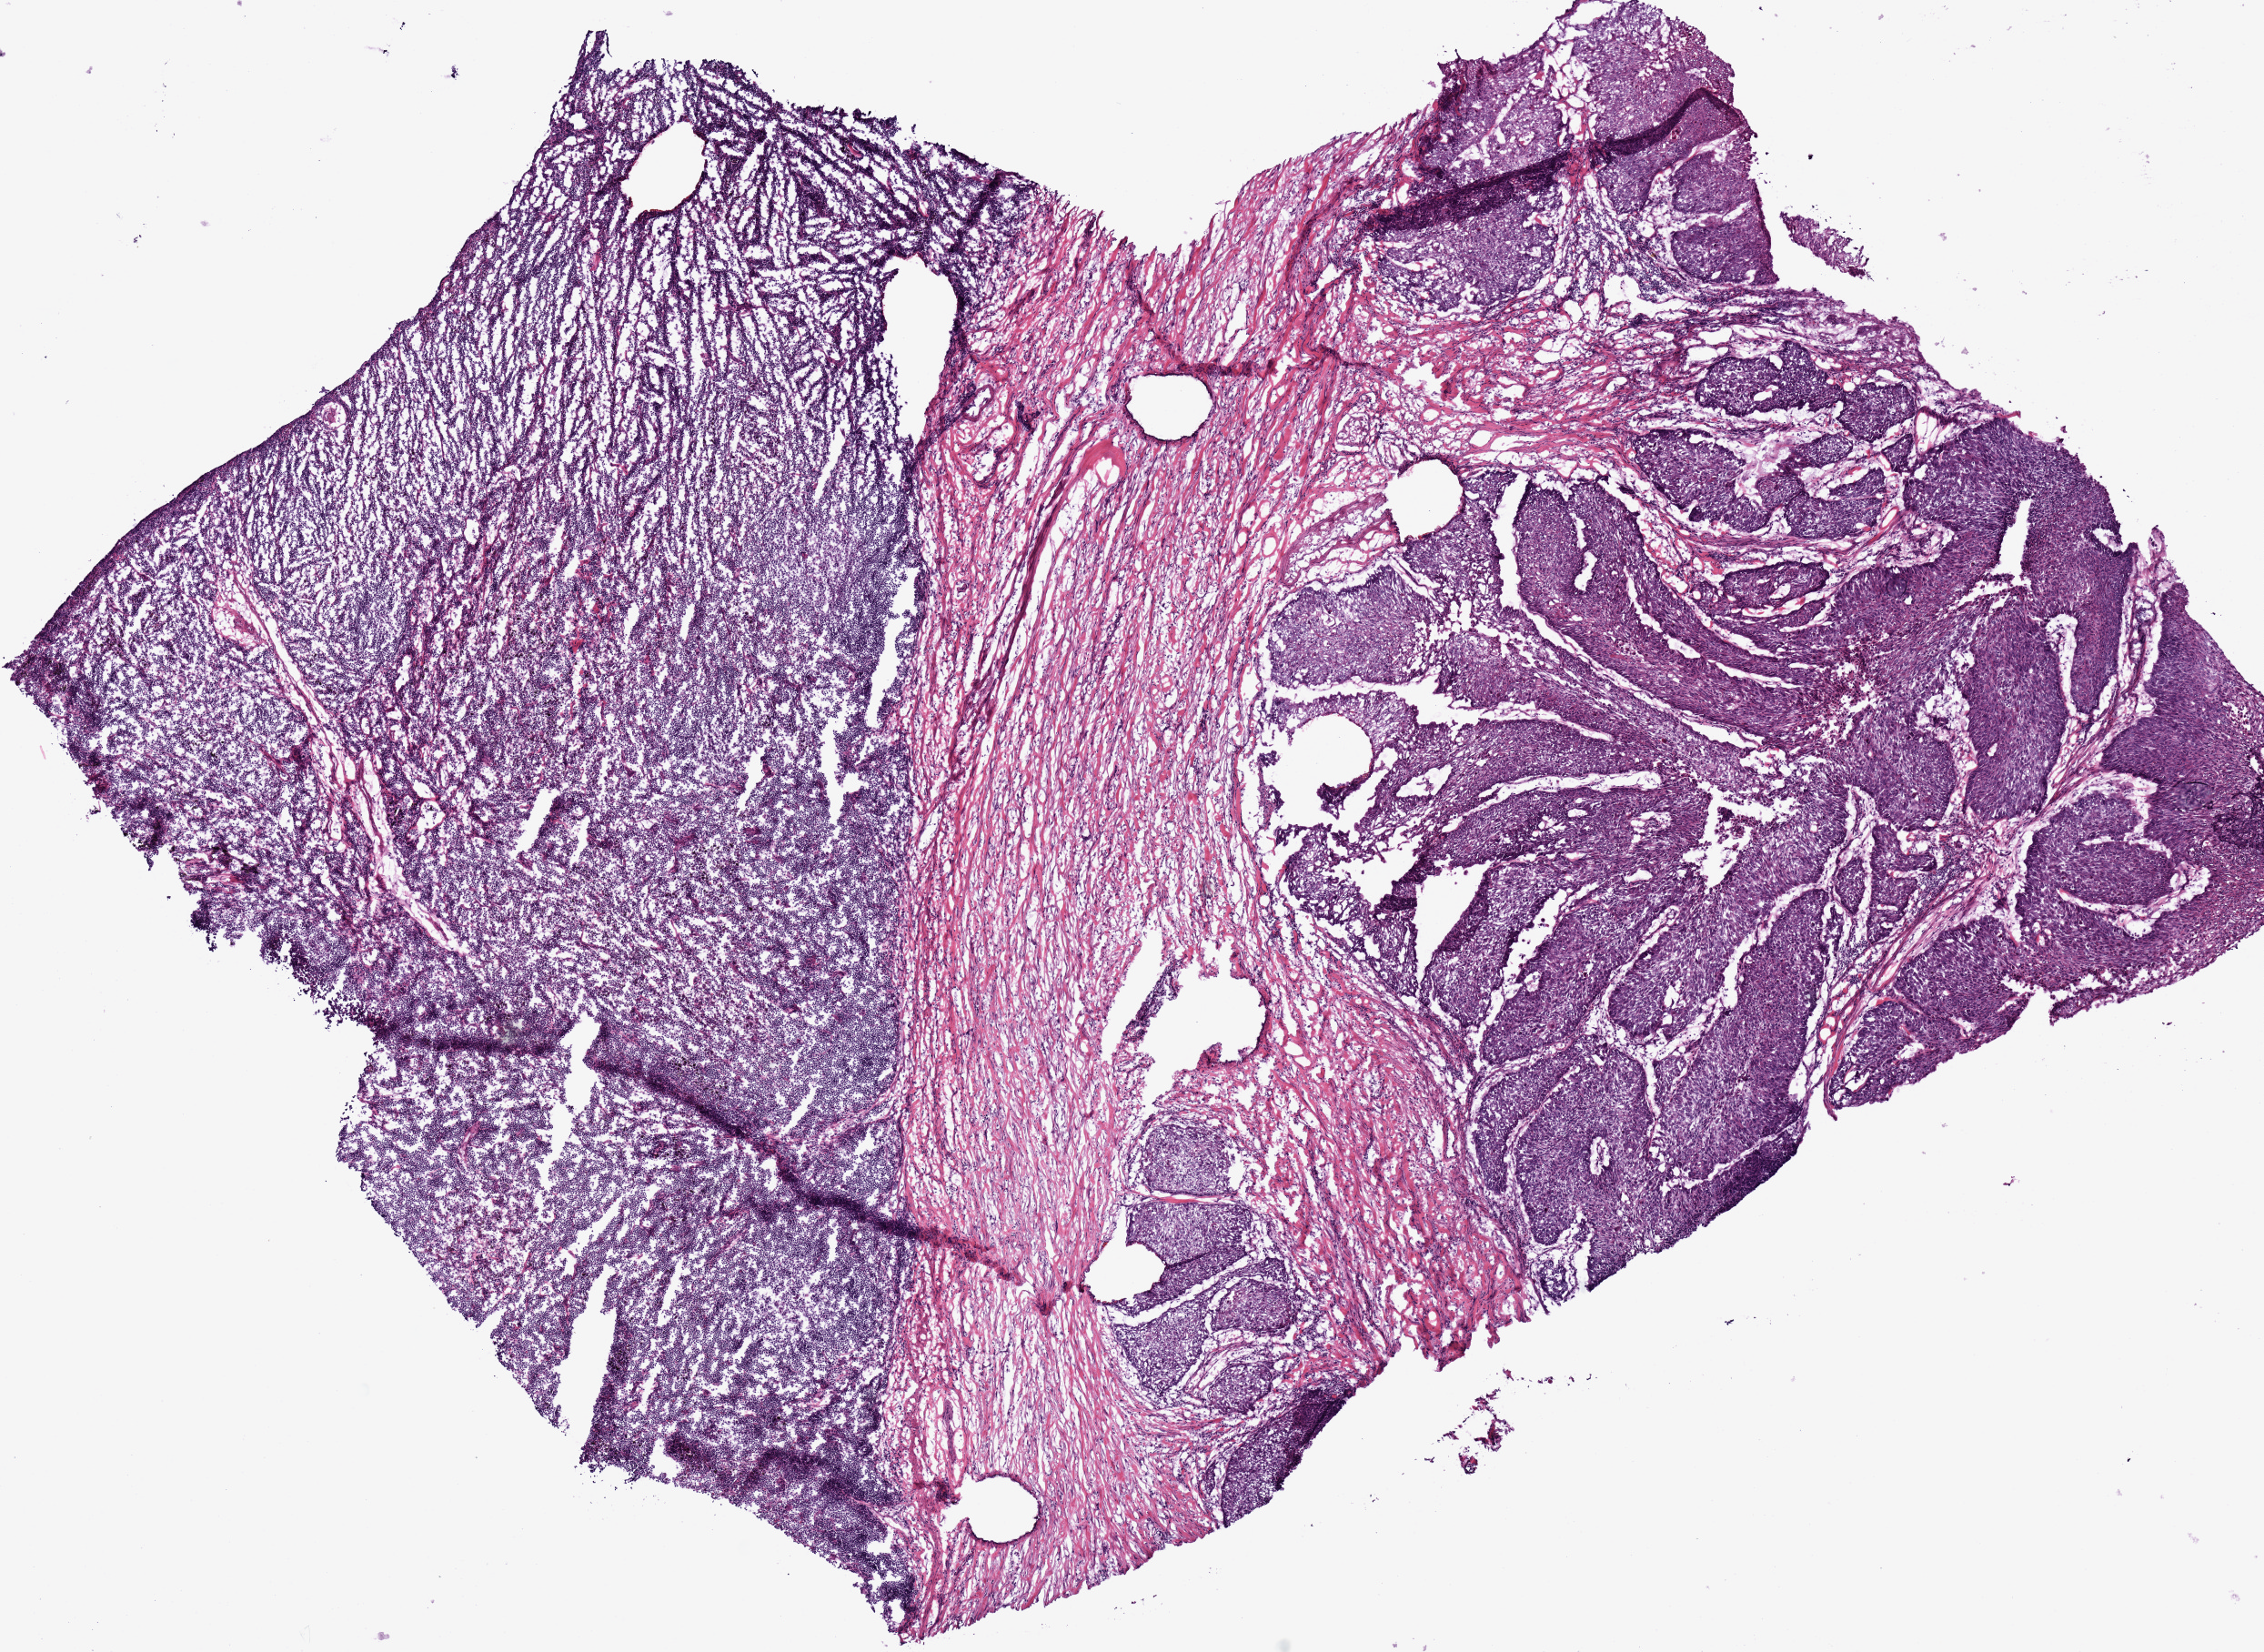
H&E-stained whole-slide image, a low-resolution overview of the entire scanned area, about 9.8 x 7.2 mm (acquisition: 20x scan). Frozen section from the top of the tissue portion. Sample: primary tumour, lung. Male, age 52 years at initial diagnosis. Pathologist review of this section (percent, as recorded): tumour nuclei 85%, necrosis 5%.
Histologic diagnosis: Squamous cell carcinoma, NOS (upper lobe, lung).